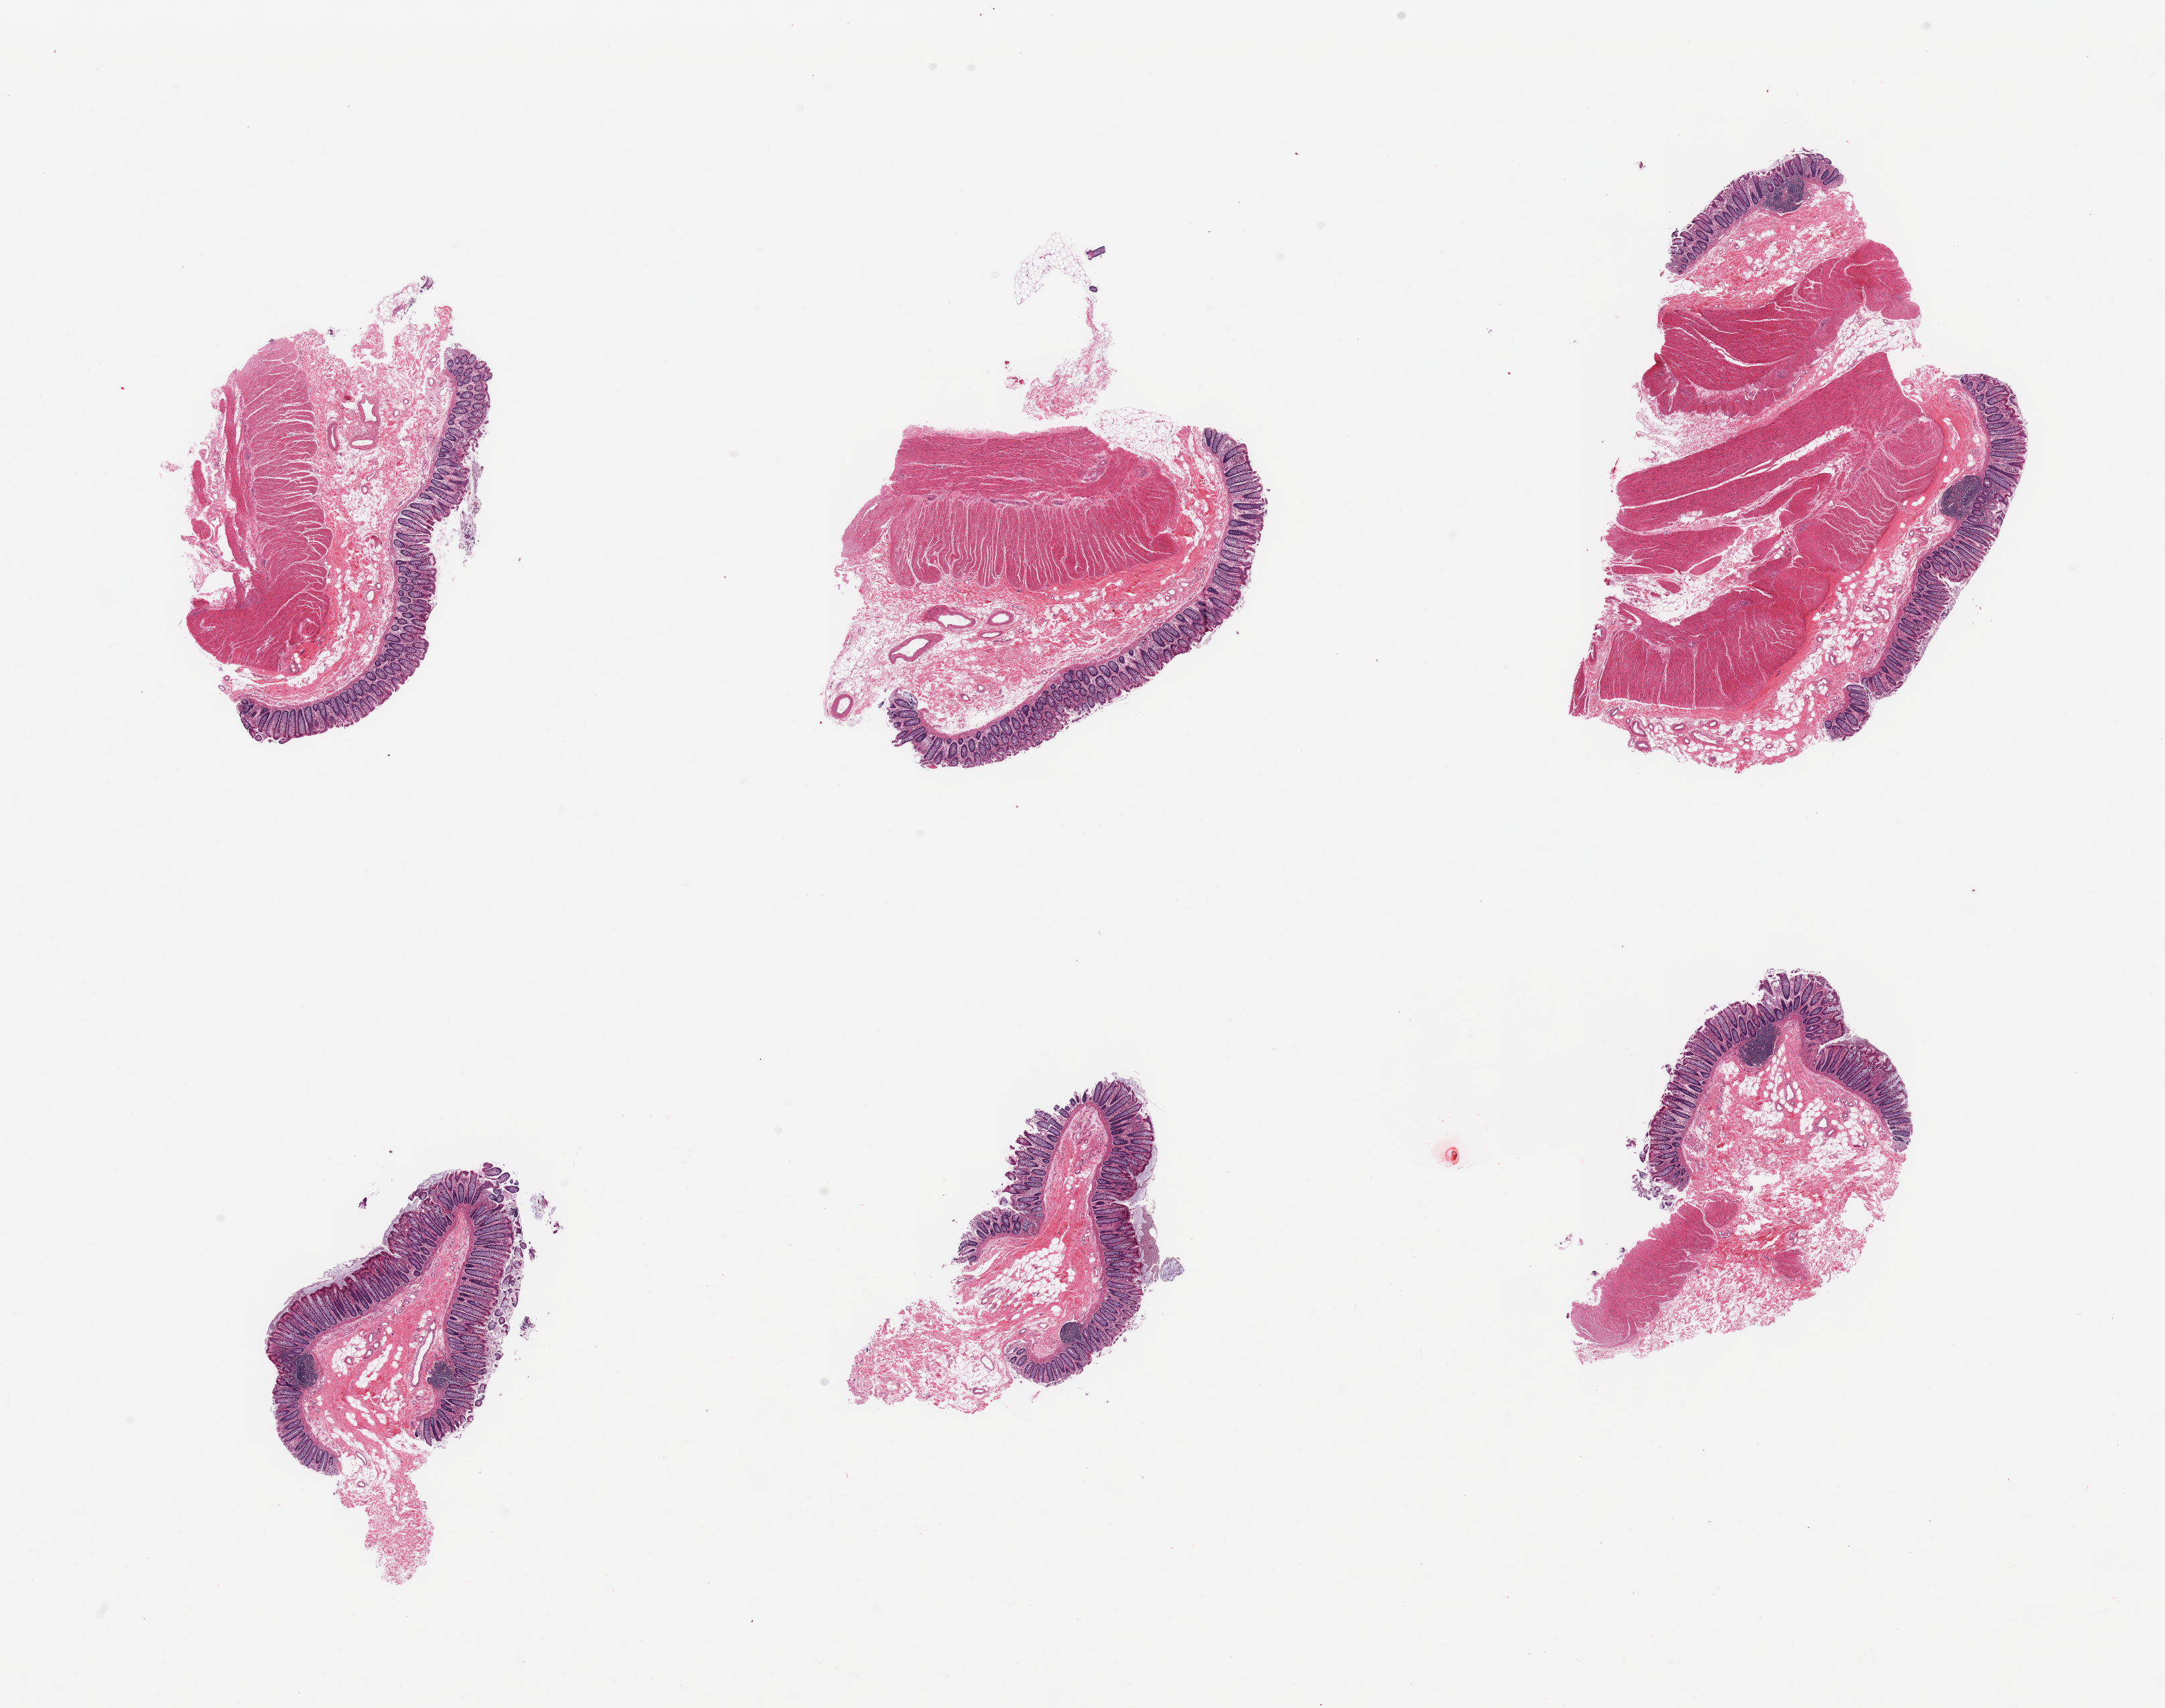
Hematoxylin and eosin (H&E) whole-slide image, brightfield, whole scanned area (about 25.6 x 20.2 mm) shown as a low-resolution overview, PAXgene-fixed, paraffin-embedded tissue, sampled site (target tissue): transverse colon, tissue donor sample. Donor sex: male.
Review note (as recorded): 6 pieces; 4 are full thickness, 2 are mucosa/submucosa only.